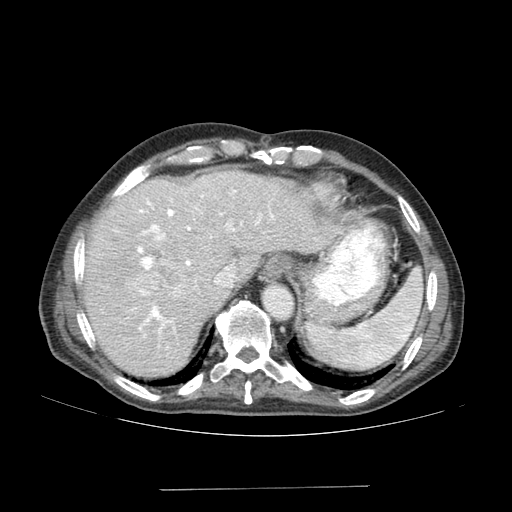
Contrast-enhanced abdominal CT (liver protocol), one axial slice. Position 128 of 192 along the scan axis. Soft-tissue window (W 400 / L 40 HU). 512 × 512 image matrix, field of view 400 × 400 mm. Case-level facts recorded for this patient, not image findings: diagnosis: hepatocellular carcinoma (patient treated with transarterial chemoembolisation; whether this scan precedes or follows treatment is not stated here); TNM stage (as recorded): Stage-IVA; Child-Pugh class: A; tumour differentiation: poorly differentiated; tumour nodularity: uninodular.
Structures marked on this image (semi-automatic segmentation, software-assisted and operator-edited):
- liver parenchyma outside the tumour (the mass and vessels are separate outlines, so this box may not span the whole liver): bounding box <84,170,338,376> (left, top, right, bottom; pixels)
- mass: <129,261,187,301>
- liver vessels: <114,190,274,337>